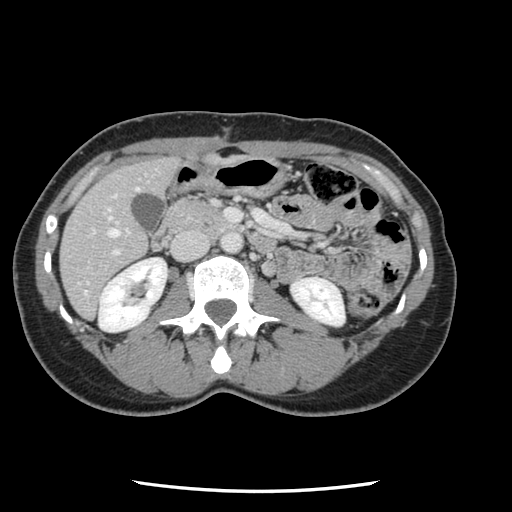
Contrast-enhanced abdominal CT, one axial slice. Soft-tissue window (W 400 / L 40 HU). 2.5 mm slice thickness. 512 × 512 image matrix, field of view 330 × 330 mm. Female patient, age 43 years. Case-level facts recorded for this patient, not image findings: diagnosis: colorectal cancer liver metastases, imaged before liver resection; multiple liver metastases: yes; largest metastasis: 3.4 cm; disease in both lobes: yes.
Outlined on this slice (outlined manually by an expert reader):
- hepatic veins: bounding box (x1, y1, x2, y2) in pixels: (108, 188, 139, 238)
- liver: (61, 158, 179, 317)
- planned liver remnant (the part of the liver to remain after resection): (61, 159, 178, 318)
- portal vein (with intrahepatic branches): (90, 202, 276, 257)